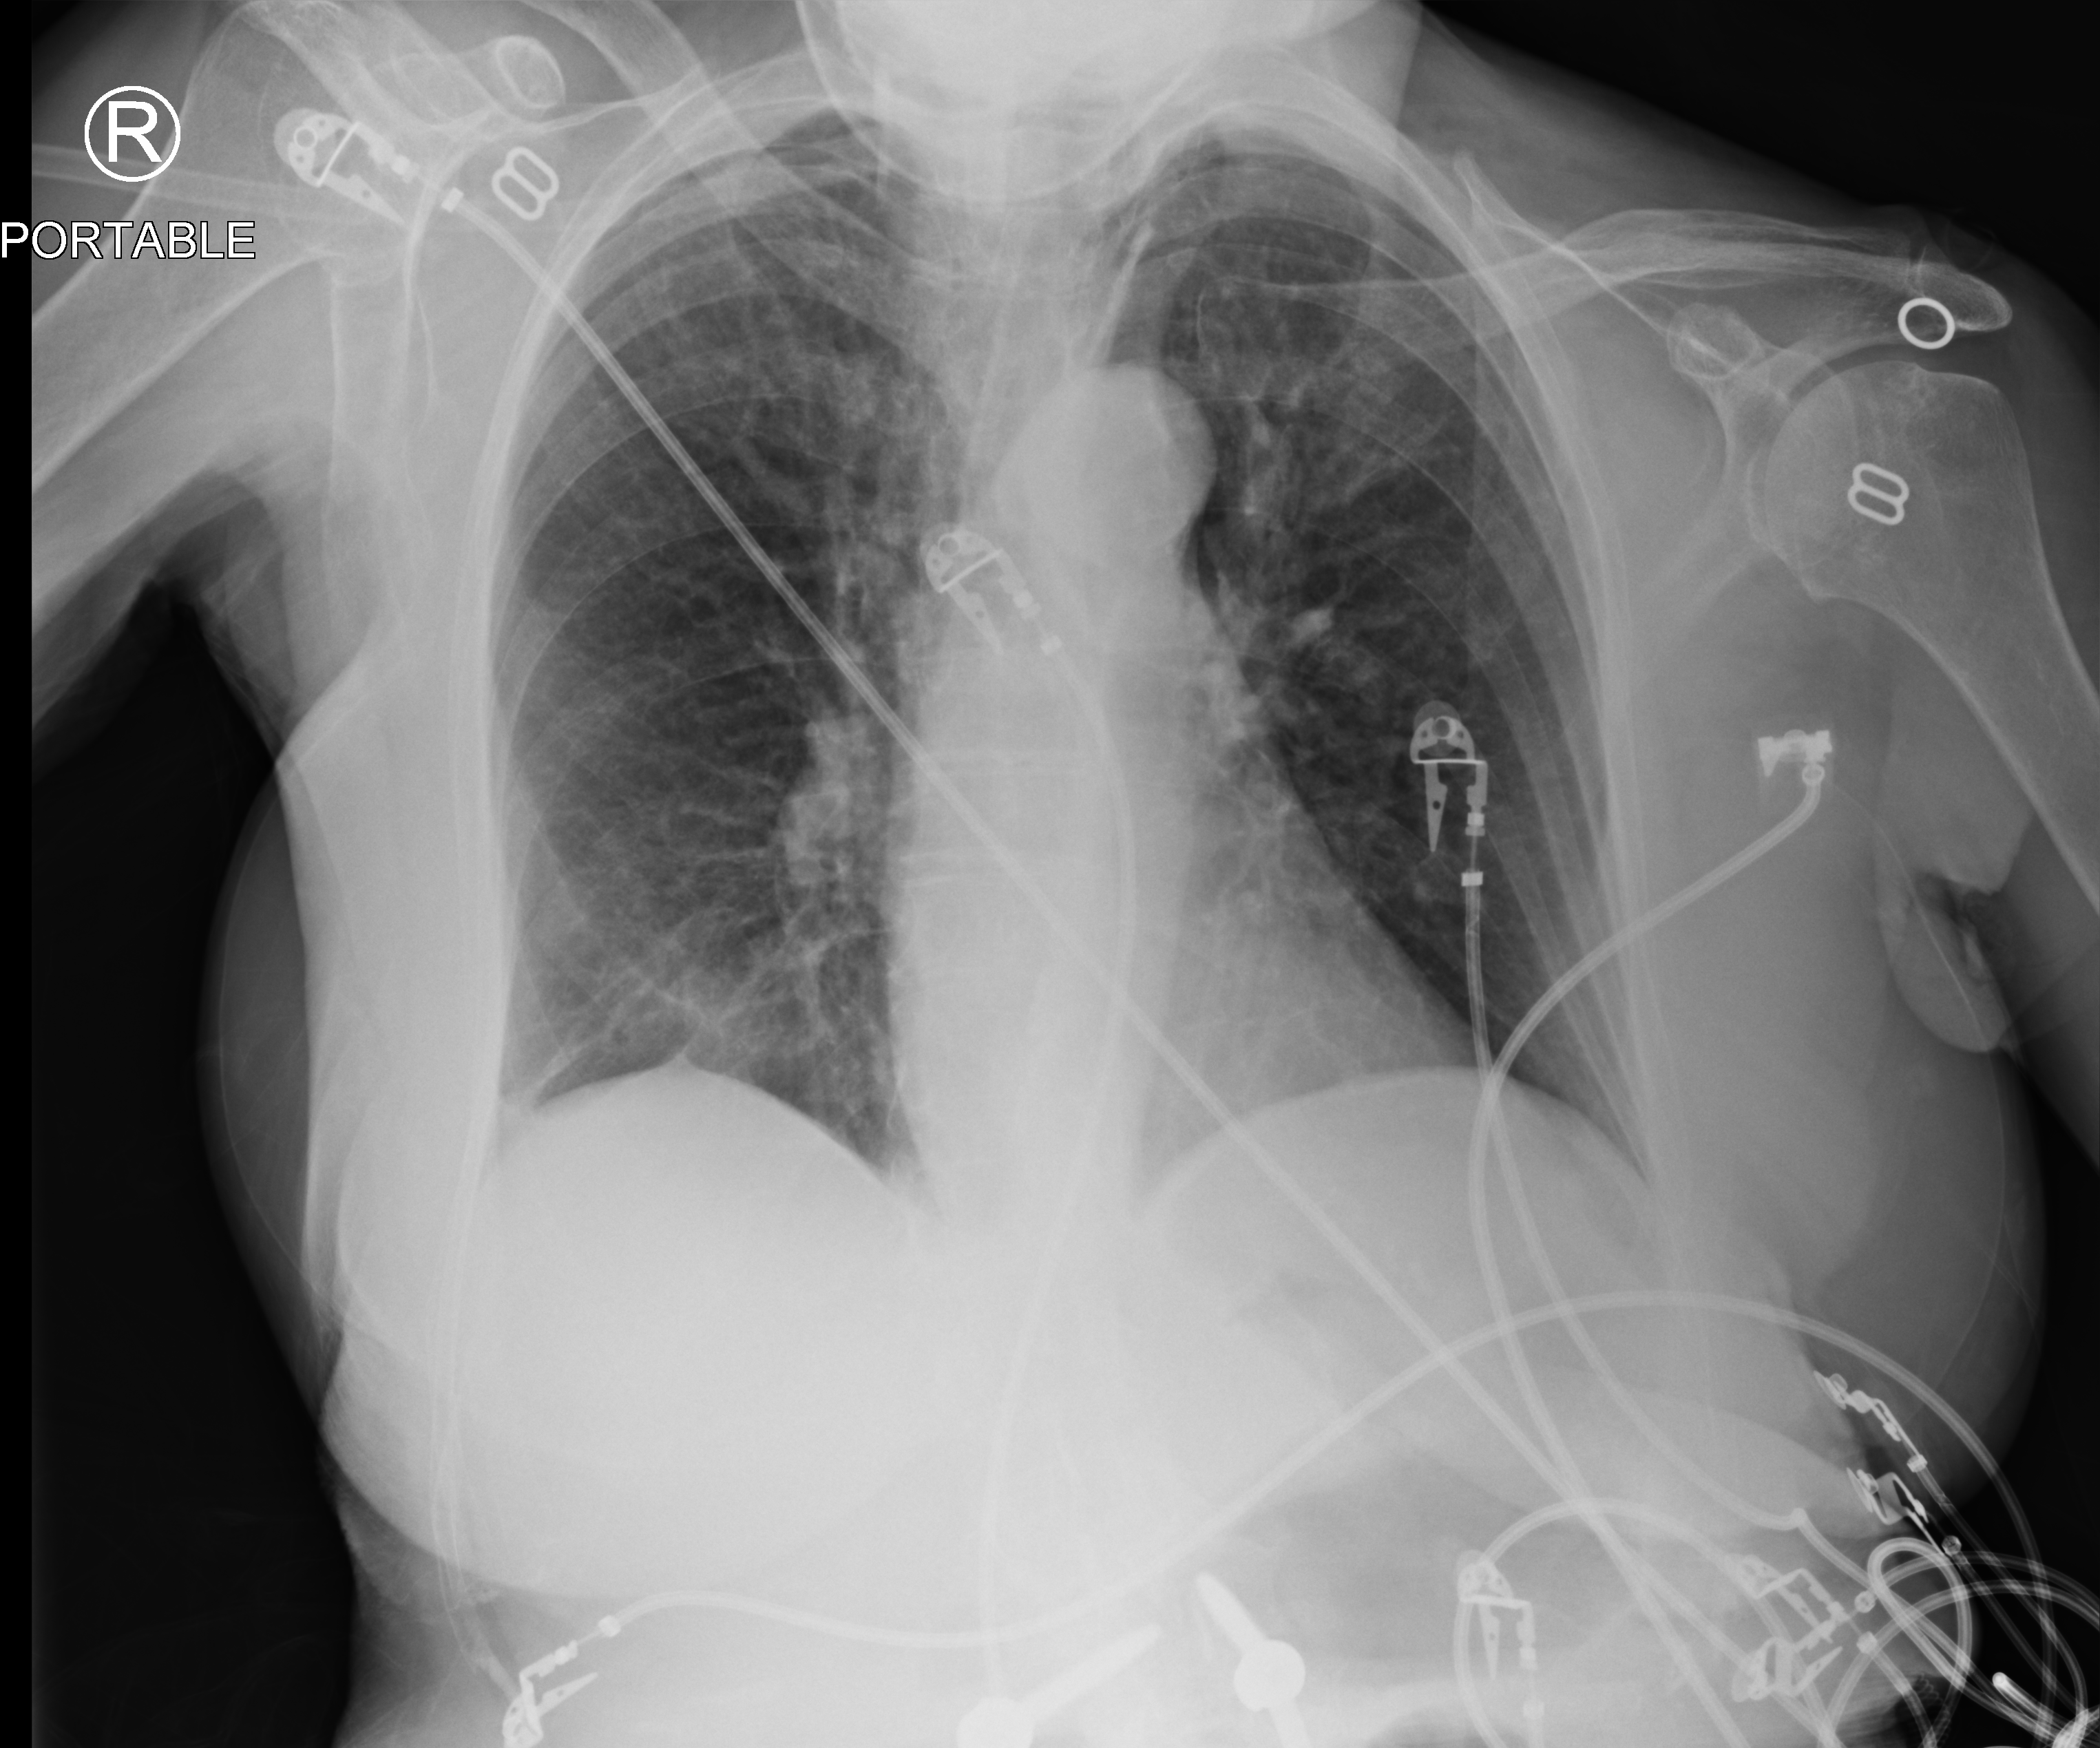
Portable chest radiograph. Female patient hospitalised with COVID-19, age 60–74 years.
Hospital-stay facts (about this admission, not read from this image; timing relative to this image not recorded):
- admitted to intensive care during this hospital stay: no
- mechanically ventilated during this hospital stay: no